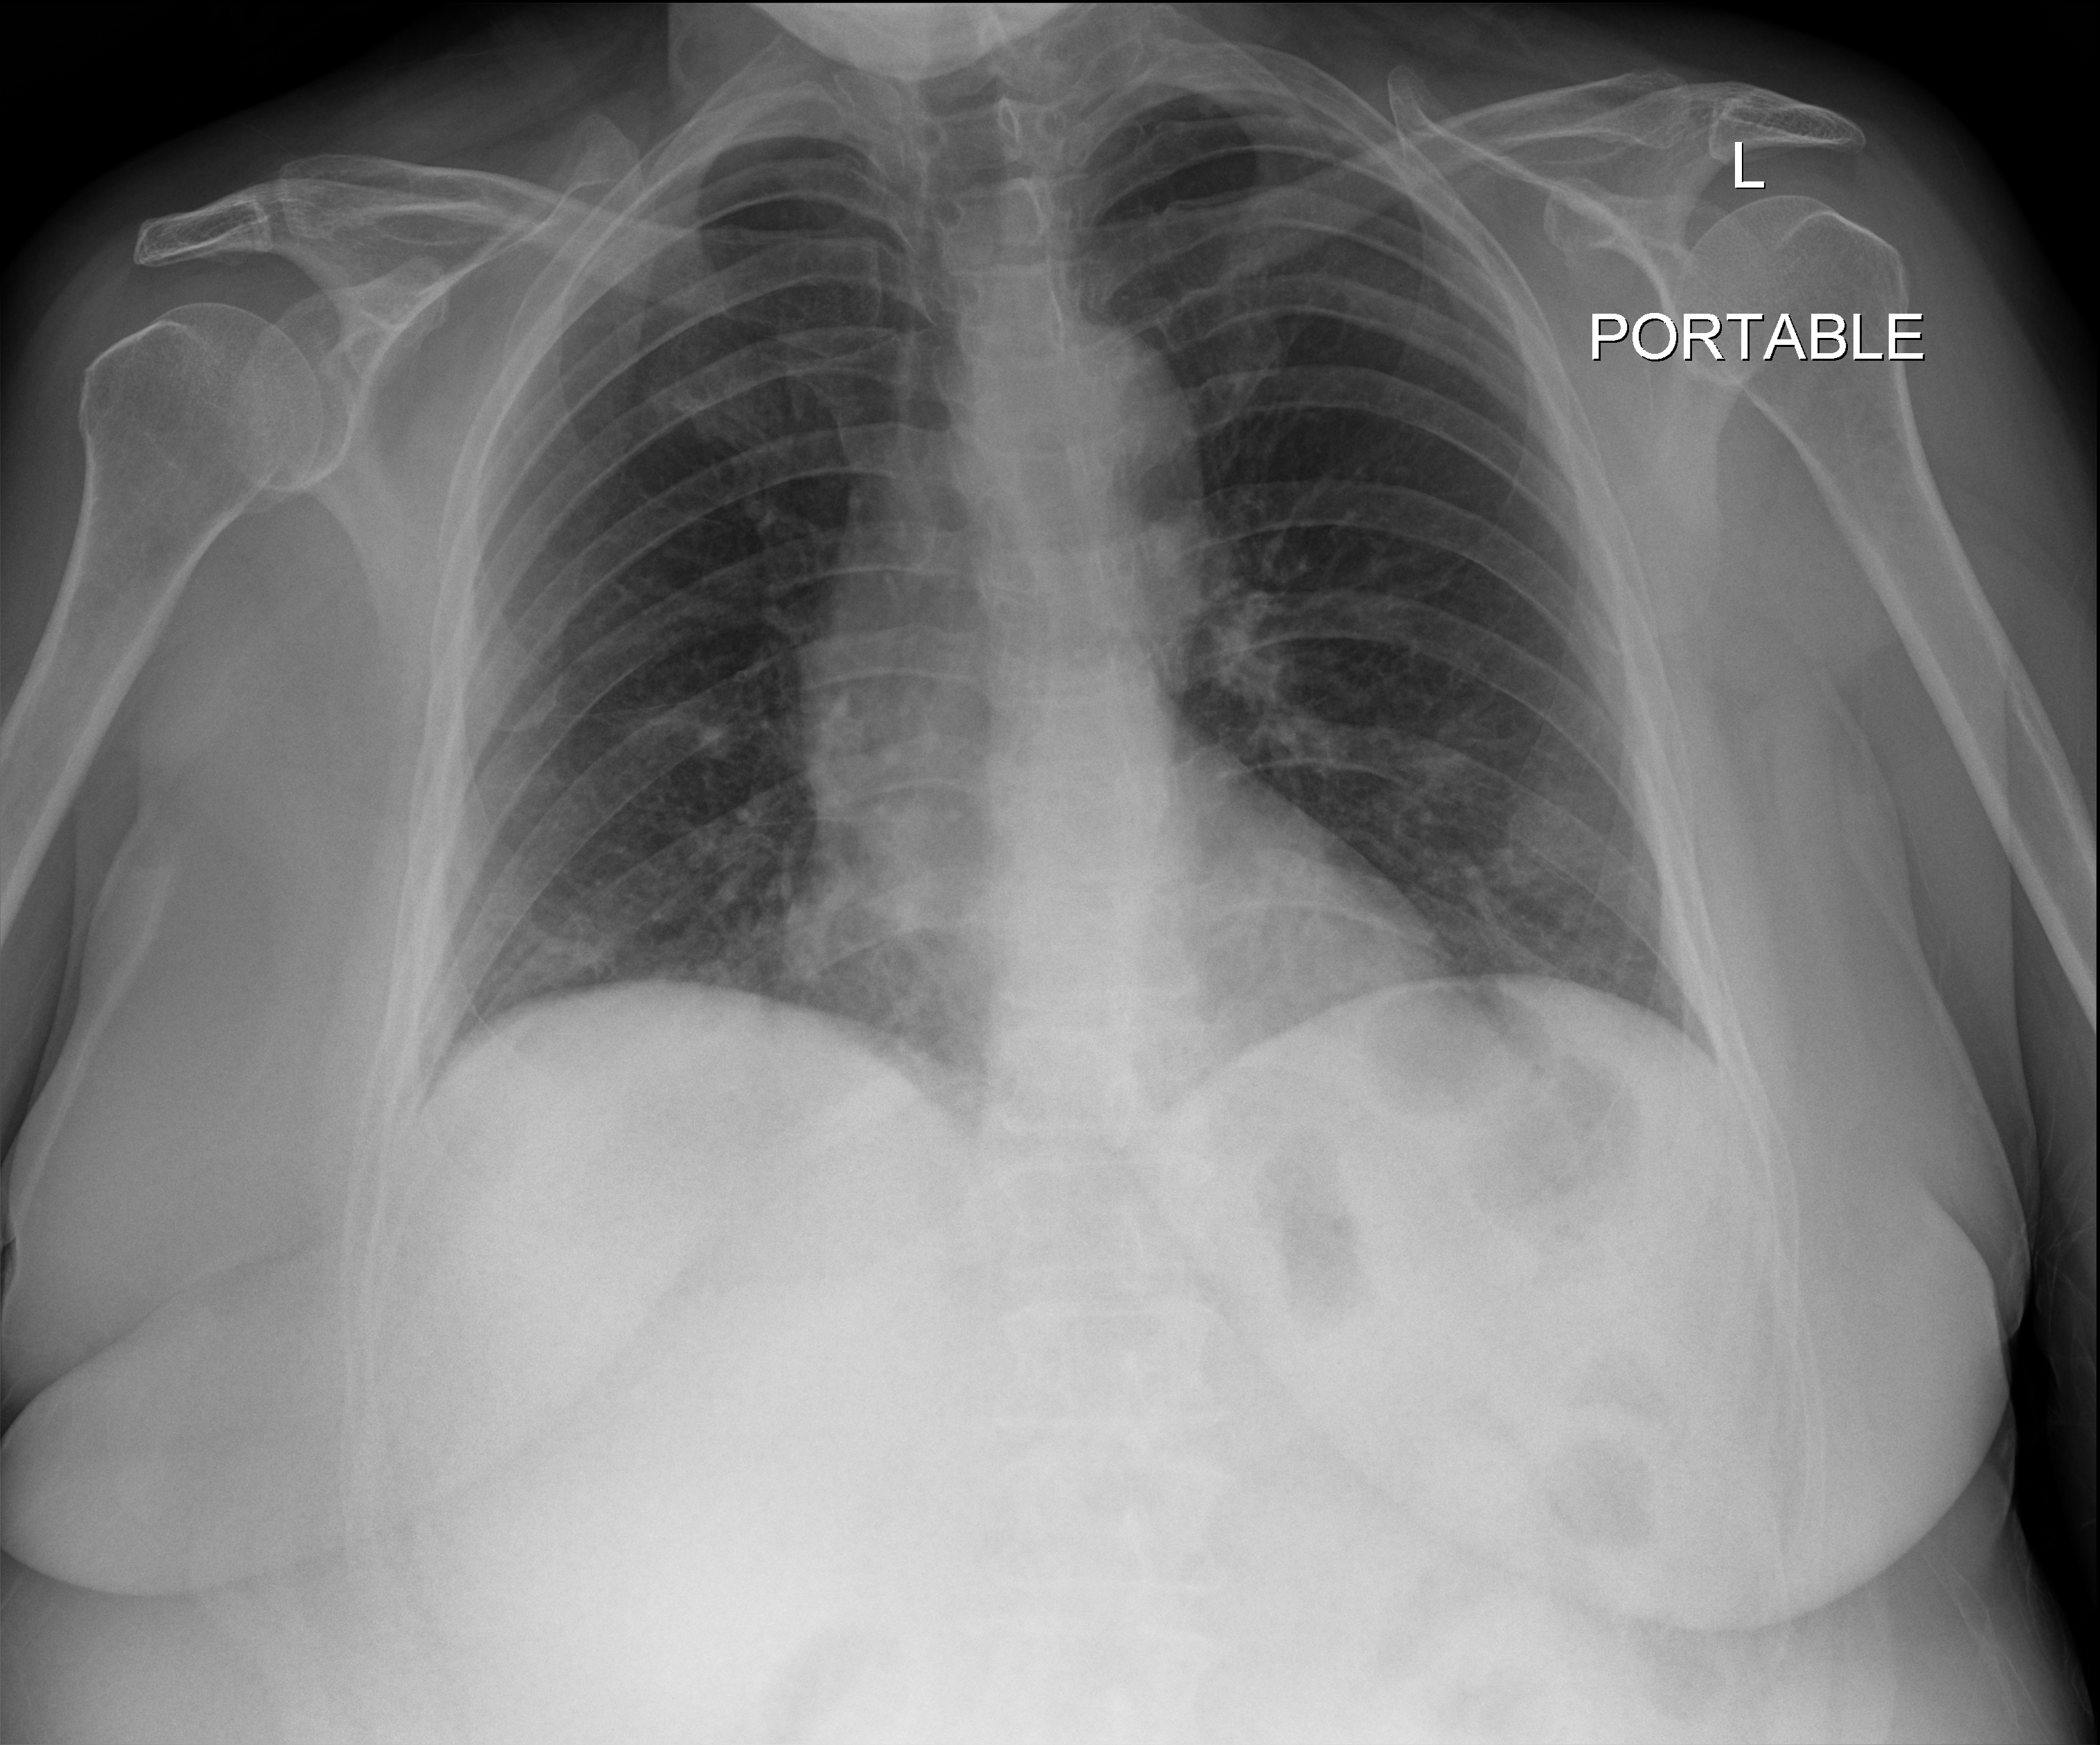
Chest radiograph (digital radiography); anteroposterior (AP) projection. Patient hospitalised with COVID-19; female, aged 60–74 years.
Admission-level facts for this patient (not findings on this image; timing relative to this image not recorded):
- length of hospital stay: 5 days
- admitted to intensive care during this hospital stay: no
- mechanically ventilated during this hospital stay: no